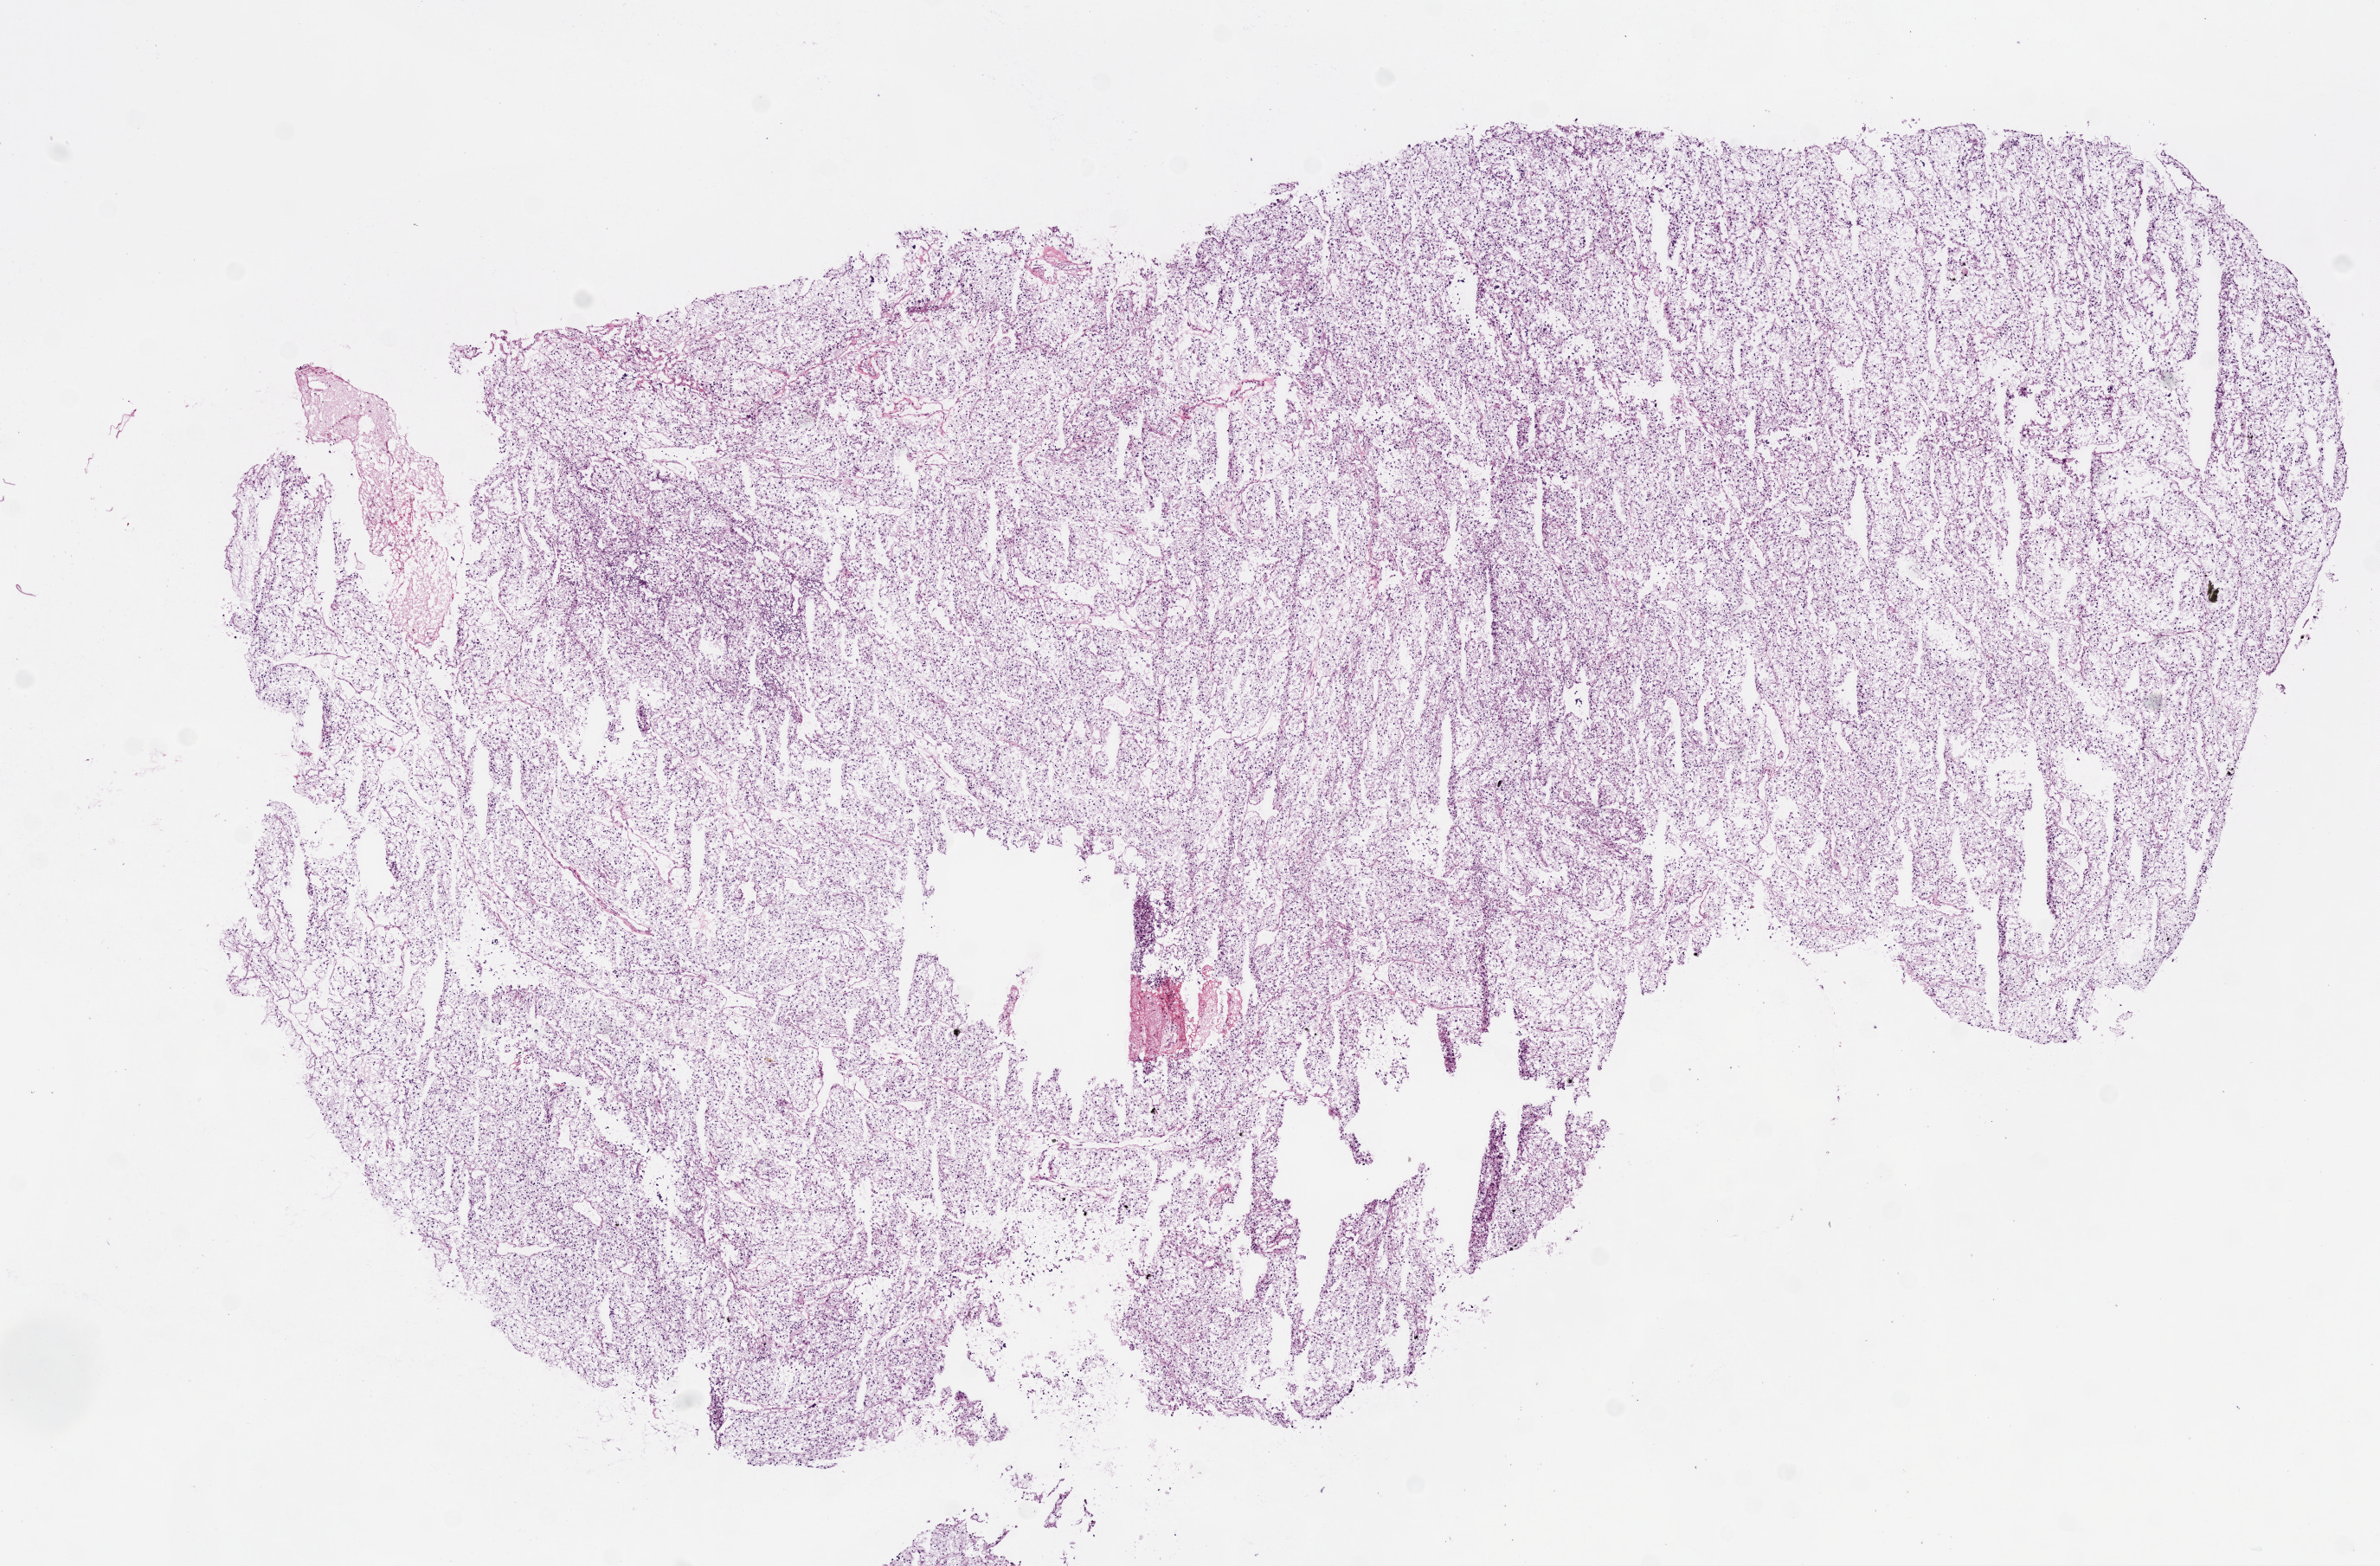
Digitized H&E tissue section (whole slide), low-resolution overview of the scanned area, about 11.0 x 7.3 mm (acquisition: 20x scan); frozen section from the bottom of the tissue portion; primary tumour sample from the kidney. Female, age 72 years at initial diagnosis. Histologic grade: G2 (moderately differentiated). Composition of this section per pathologist review: tumour cells 100%, tumour nuclei 95%, necrosis 0%. Infiltration values recorded for this section: lymphocyte infiltration 1%.
- laterality: left
- AJCC pathologic stage: I
- pathologic diagnosis: Clear cell adenocarcinoma, NOS